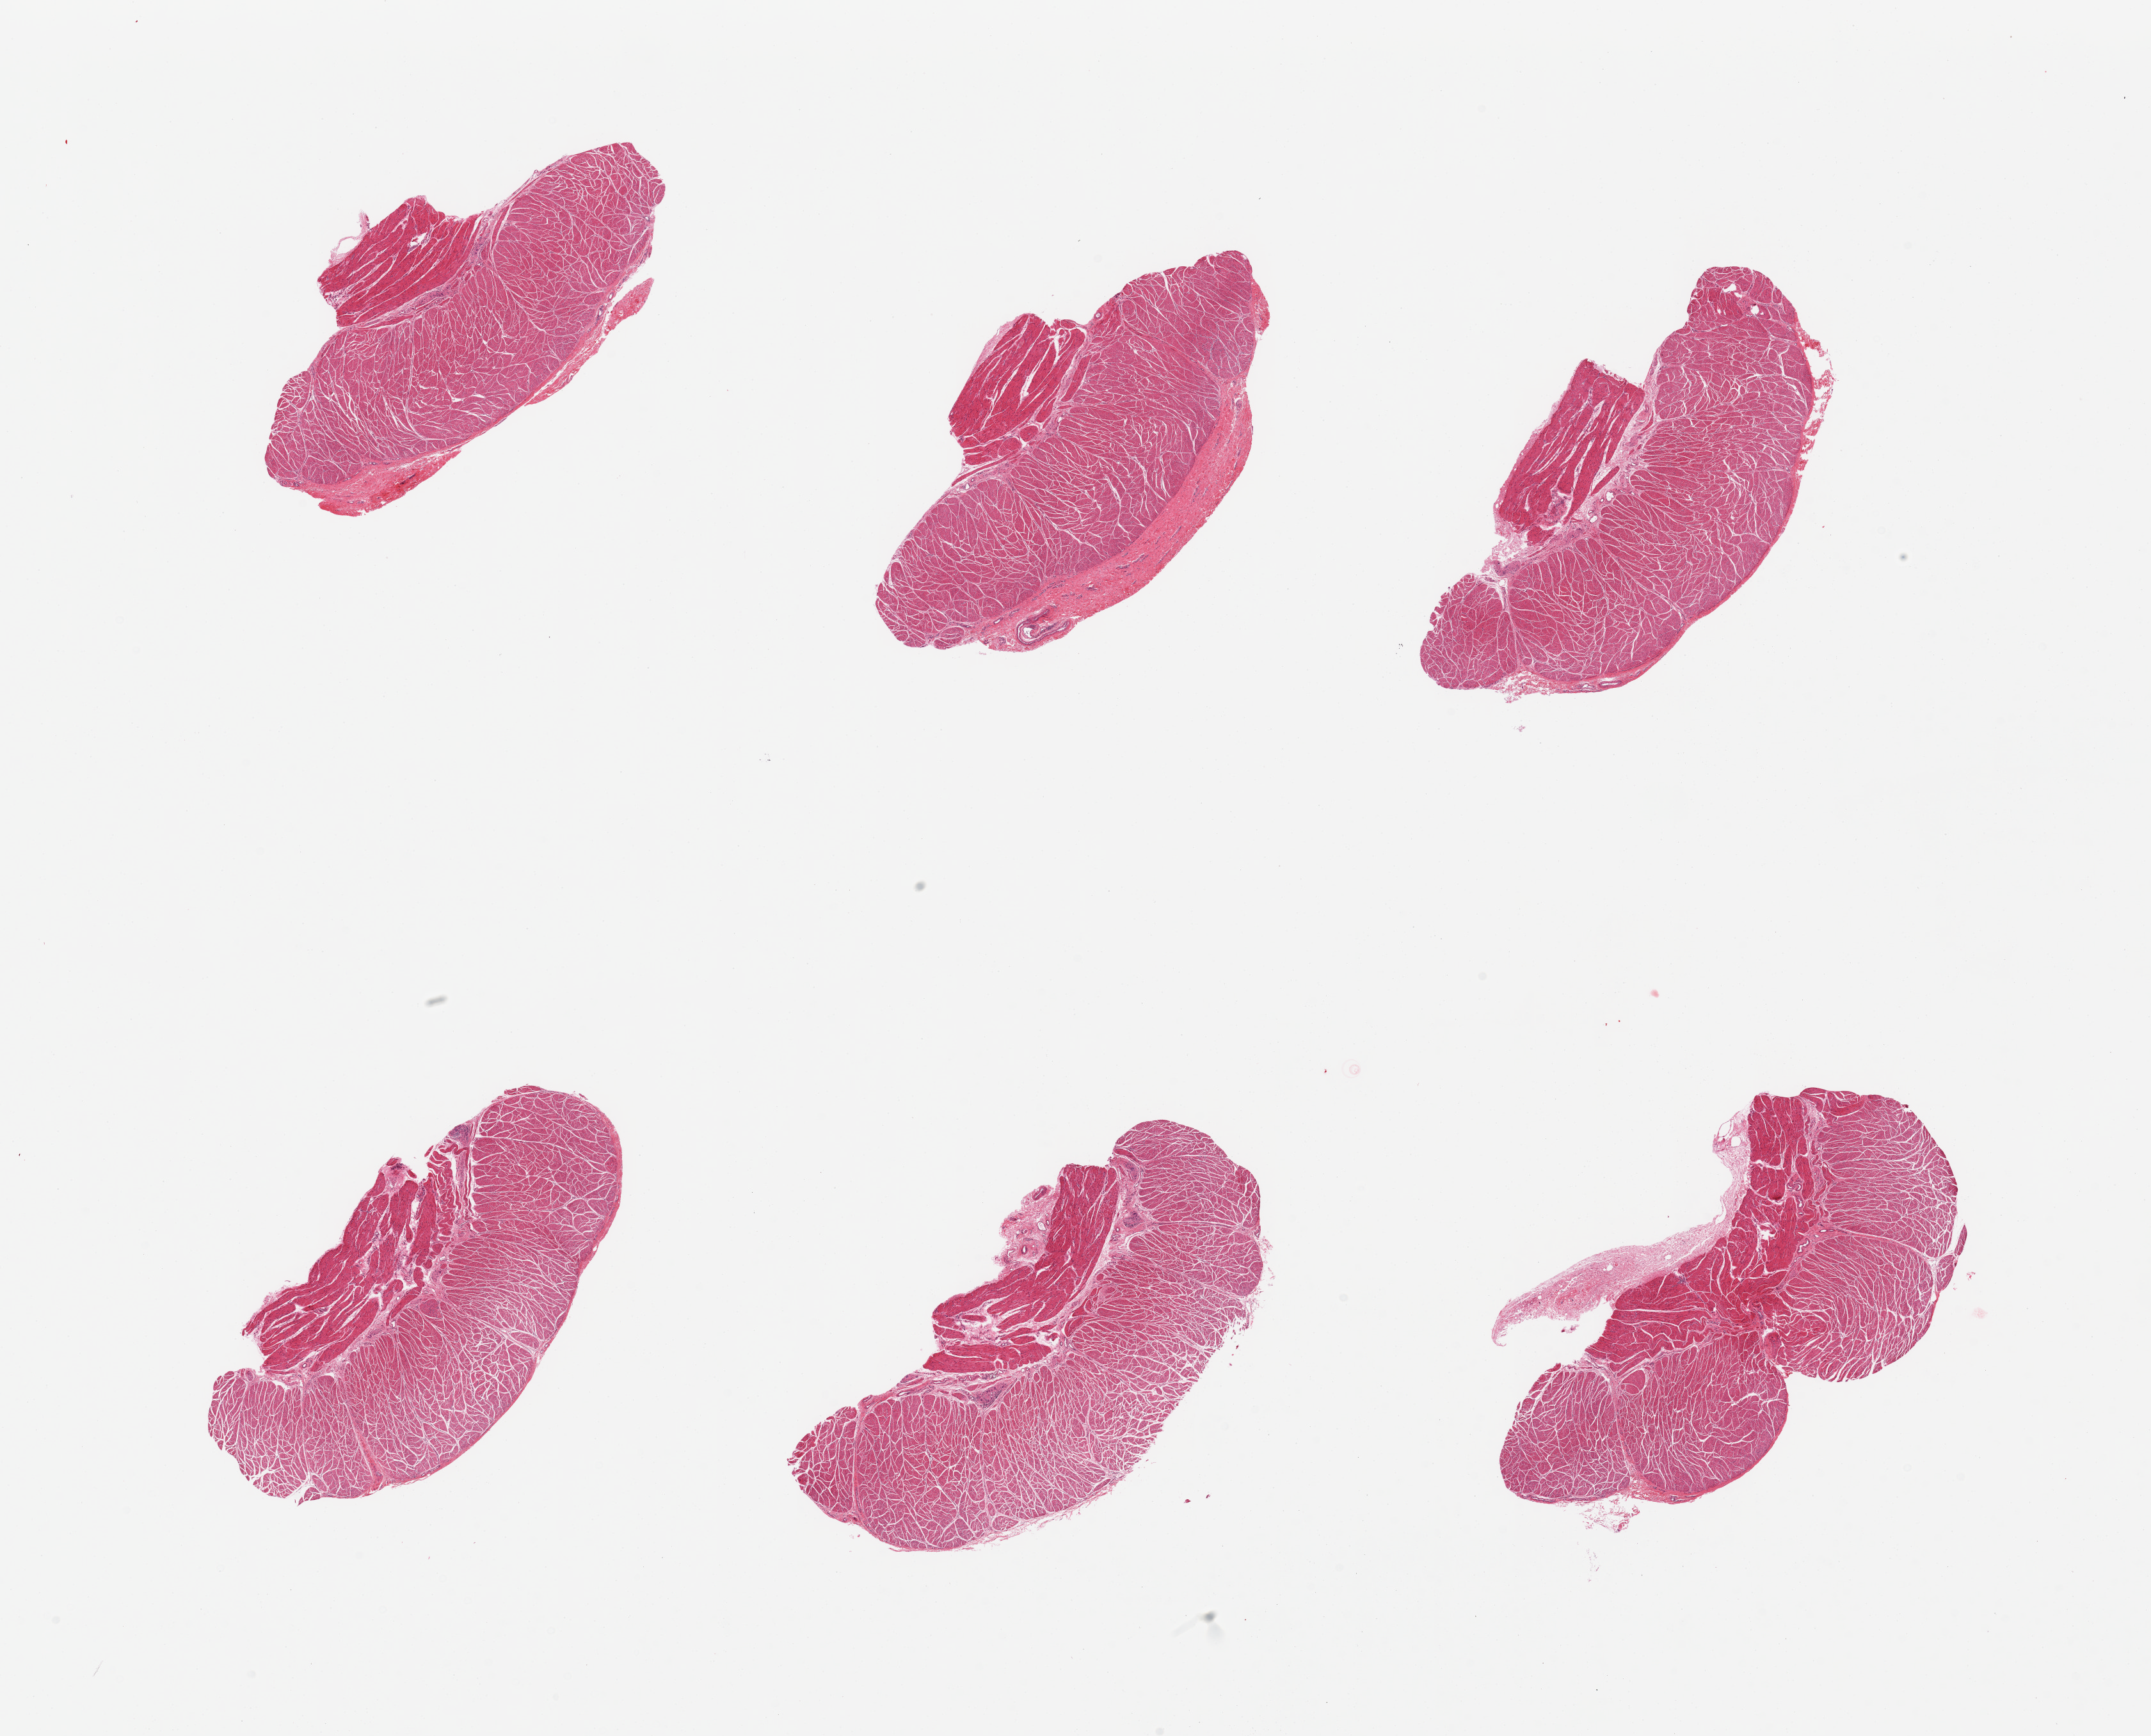
Digitized H&E-stained section, low-resolution overview of the scanned area, about 26.6 x 21.5 mm; PAXgene-fixed paraffin-embedded (PFPE) section; target tissue: esophageal muscle; donor tissue sample.
- pathologist's review note for this sample: 6 pieces, all muscularis; focal stromal connective tissue